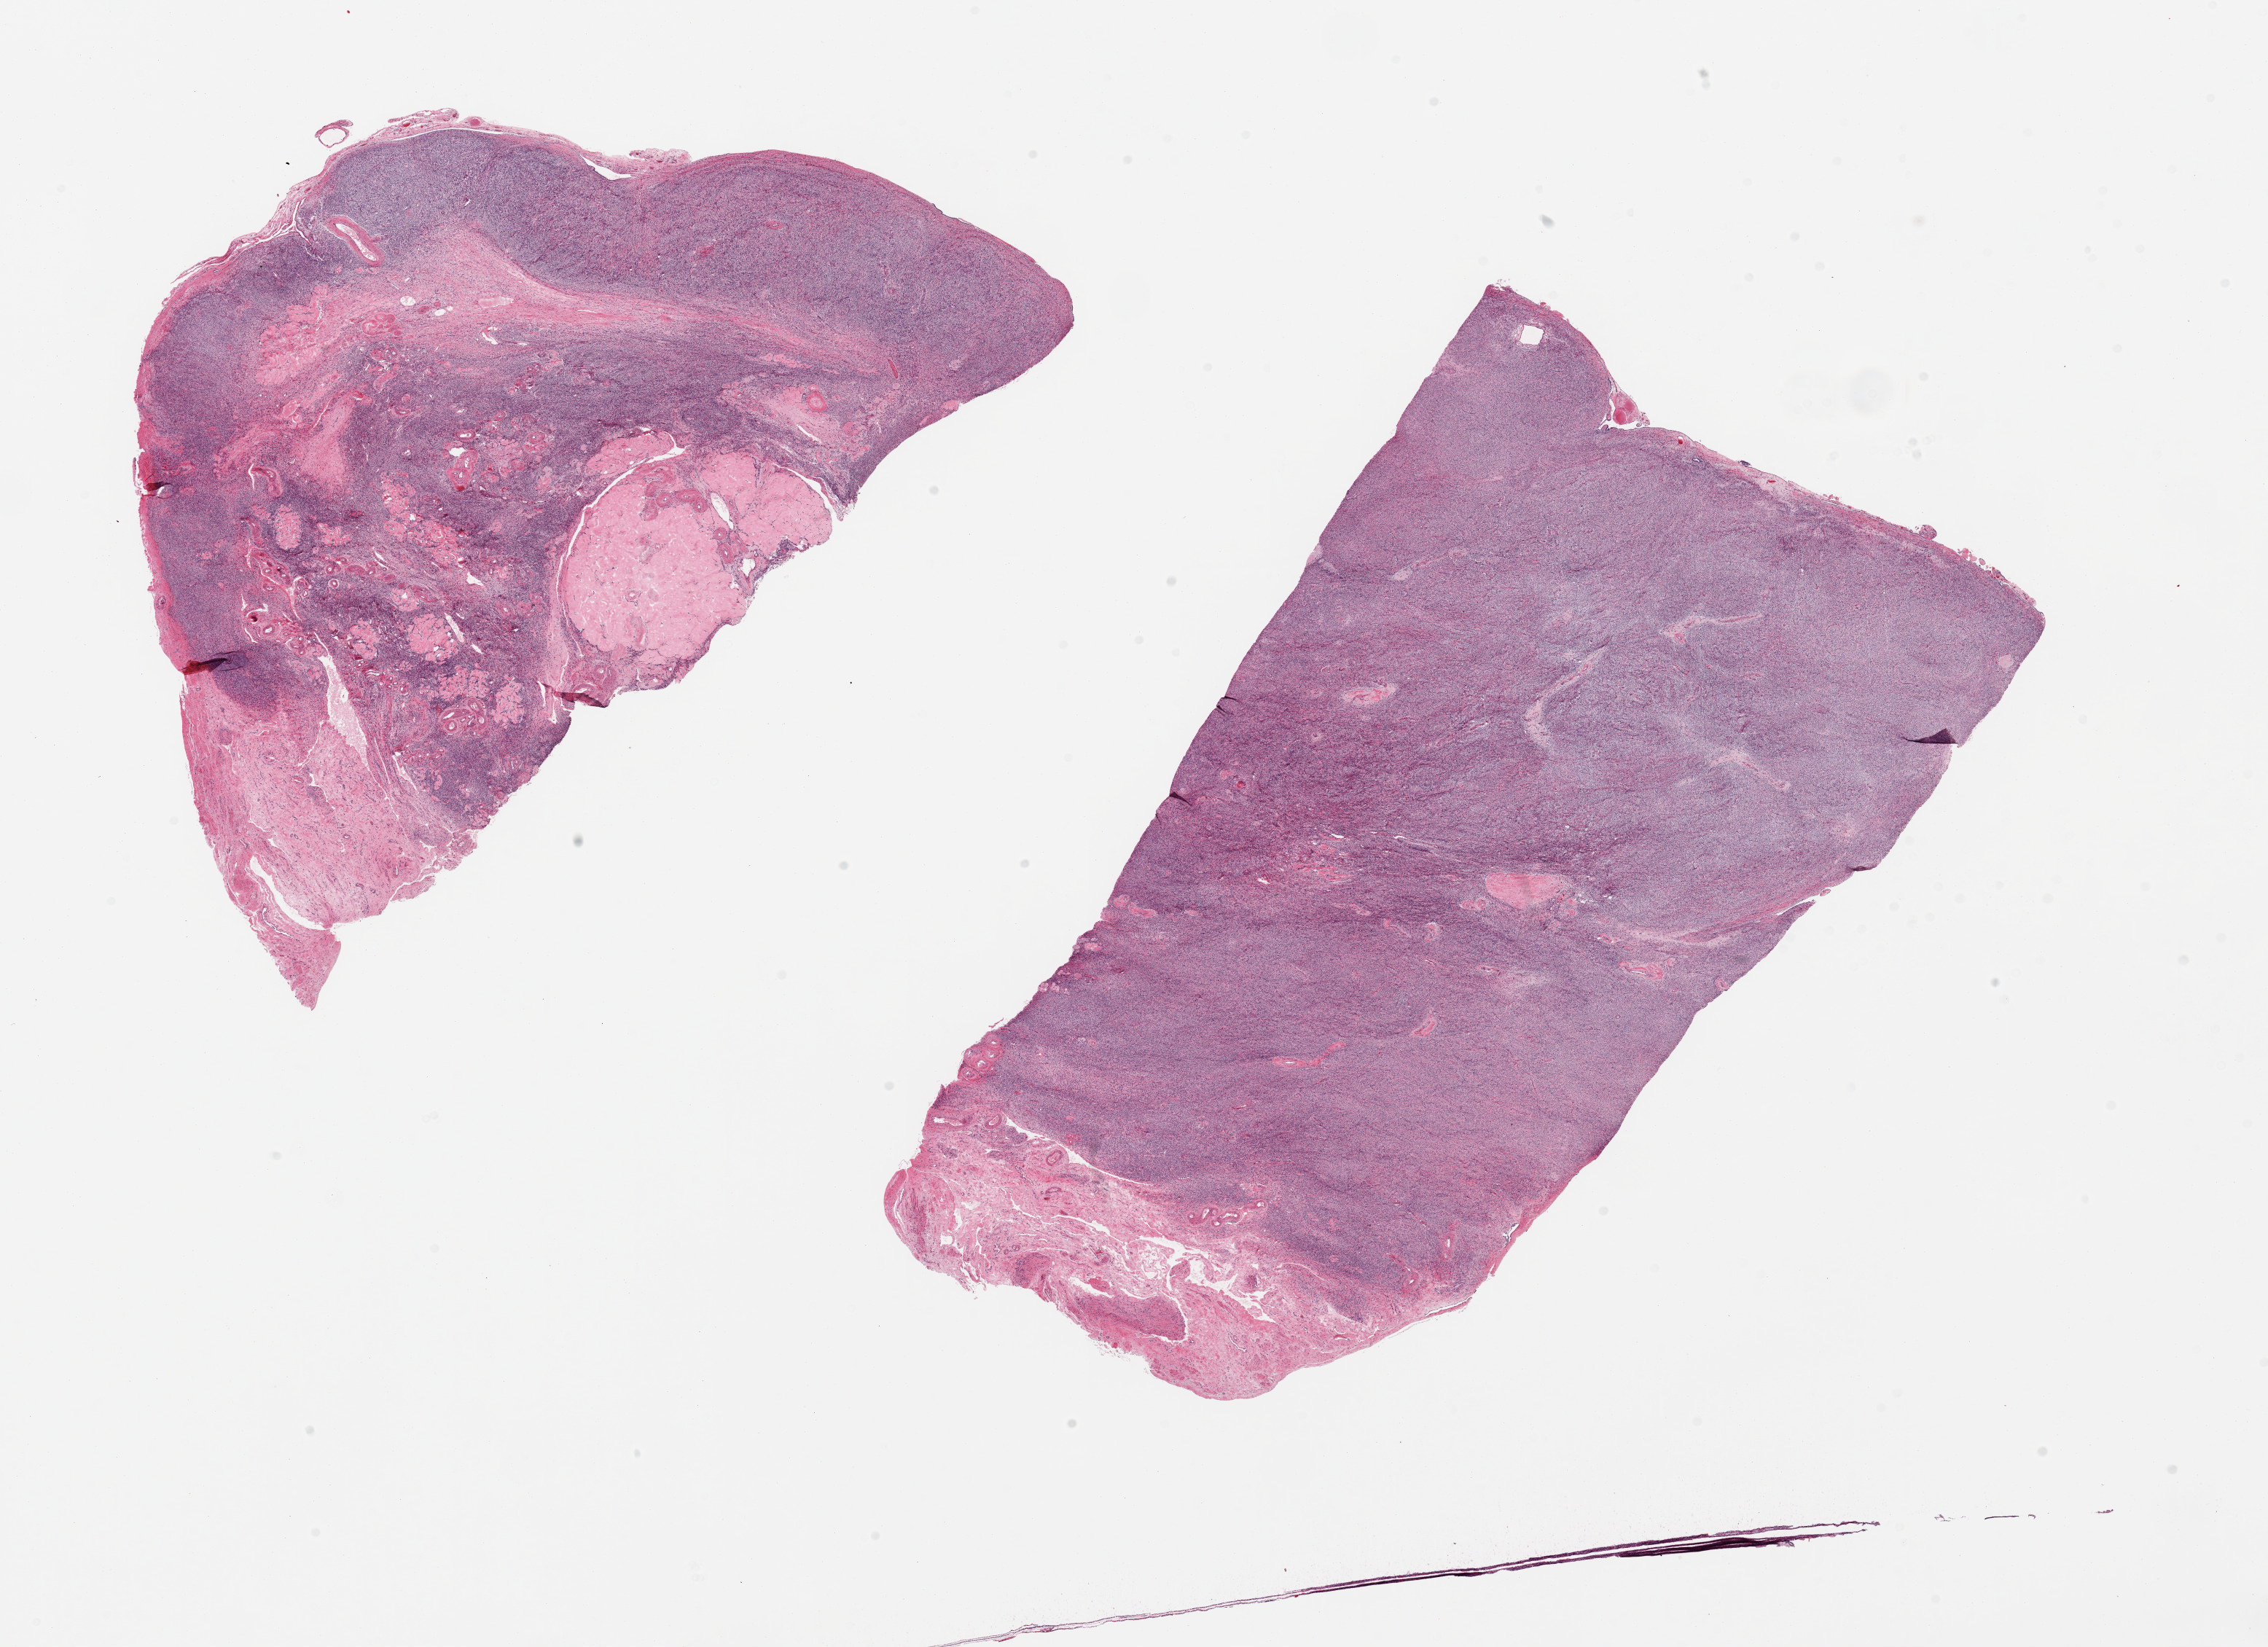
Whole-slide image, haematoxylin and eosin stain, shown as a low-resolution overview of the whole scanned area (about 24.6 x 17.9 mm). PAXgene-fixed, paraffin-embedded tissue. Sampled site (target tissue): ovary. Tissue donor sample. Donor sex: female.
Reviewer comment on this tissue sample: 2 pieces; atrophic with corpora albicantia.